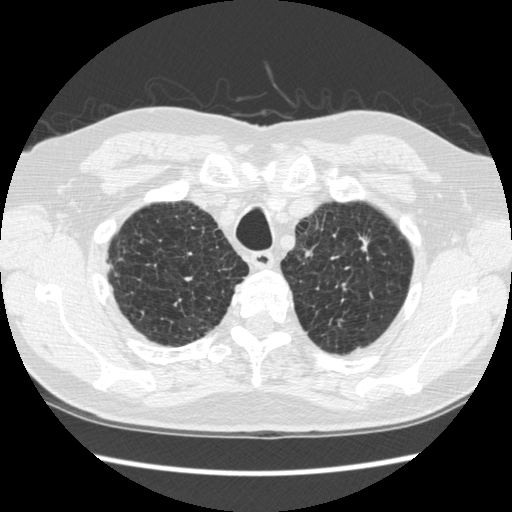
Axial slice from a low-dose chest CT screening exam. Second annual screen. Lung window (W 1500 / L -600 HU). 1.25 mm slice thickness. Standard (soft-tissue) reconstruction kernel (STANDARD). 120 kVp. Slice 46 of 295 in the series. 512 × 512 image matrix, field of view 348 × 348 mm. Male participant, aged 70 years at enrolment. Former smoker at enrolment.
Lesion marked by an expert reader, bounding box (x1, y1, x2, y2) in pixels: (331, 219, 392, 287). The screening reader recorded 5 non-calcified nodules or masses ≥4 mm on this exam; which of them this box marks is not recorded. Official screen result: positive, change unspecified: nodule(s) >= 4 mm or enlarging nodule(s), mass(es), or other non-specific abnormalities suspicious for lung cancer. Later outcome: lung cancer diagnosed 479 days after this screen (after the third annual screen) — squamous cell carcinoma, NOS, left upper lobe, moderately differentiated (G2), stage IA (AJCC 6th edition), 18 mm at pathology.